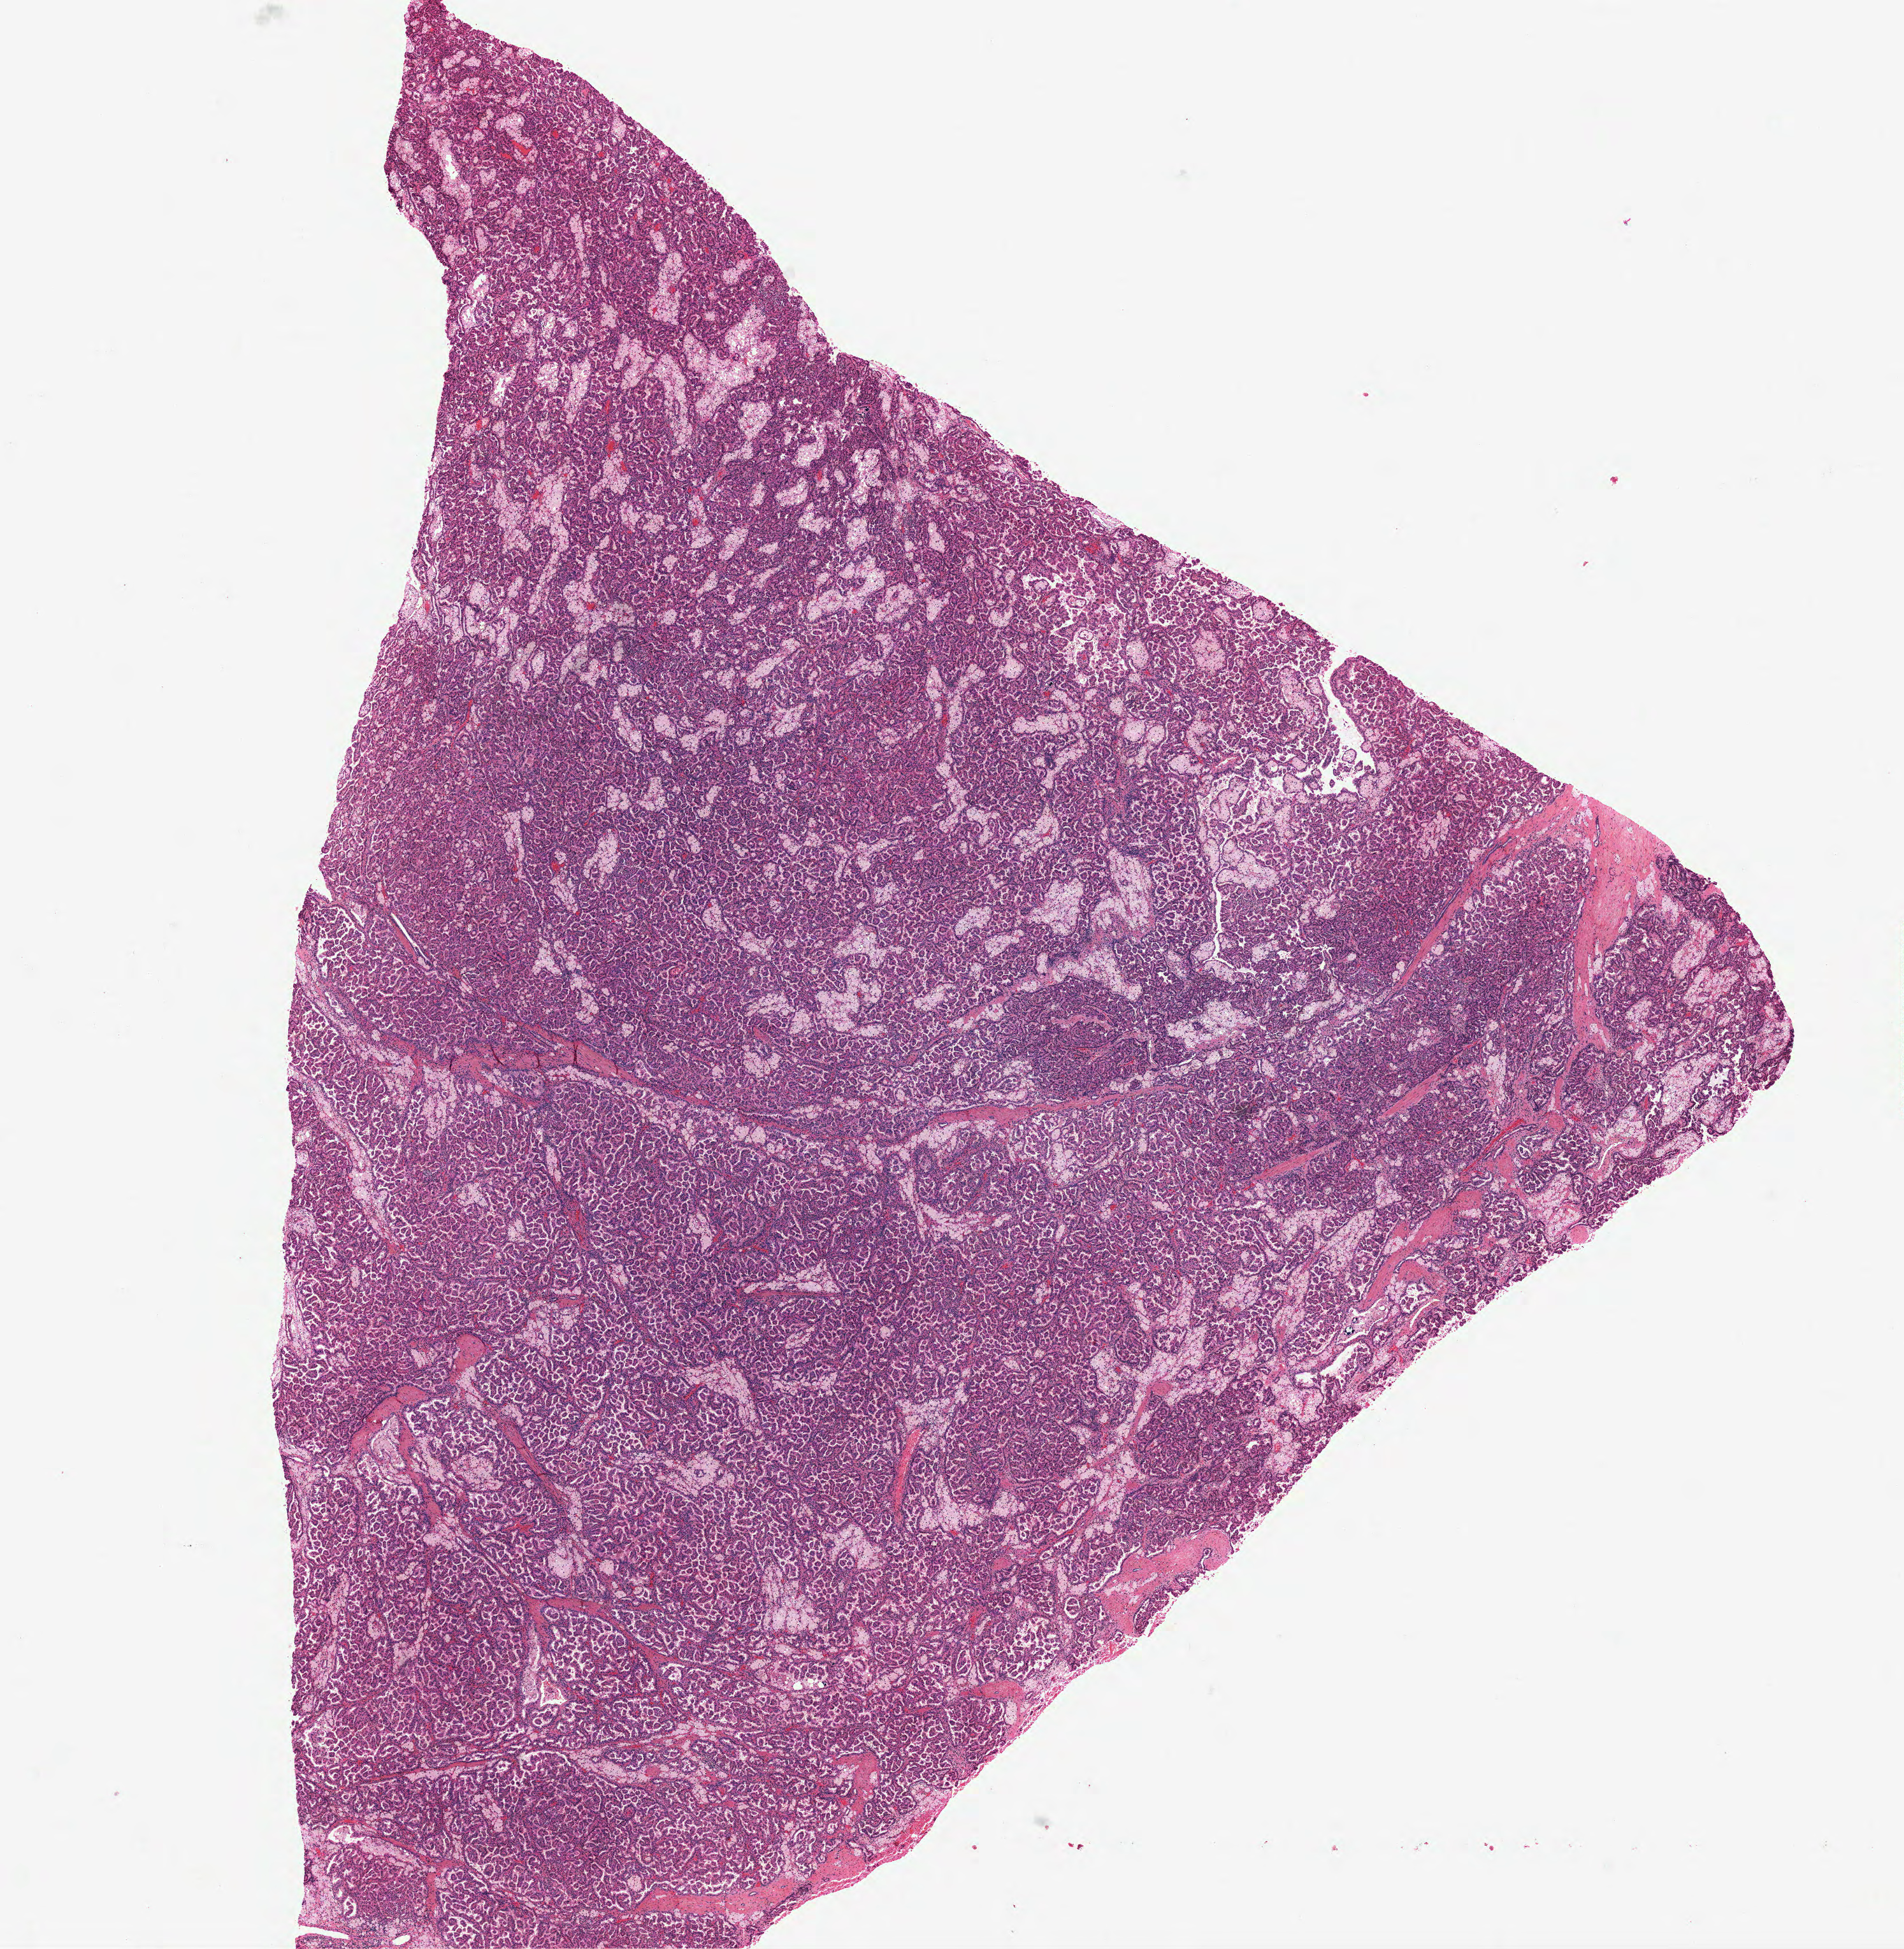
H&E whole-slide image — low-resolution overview of the scanned area, about 12.0 x 12.3 mm (slide scanned at 40x), formalin-fixed paraffin-embedded (FFPE) diagnostic section, sample: primary tumour, kidney. Male patient; age at initial diagnosis 49 years.
Pathologic diagnosis: Papillary adenocarcinoma, NOS.